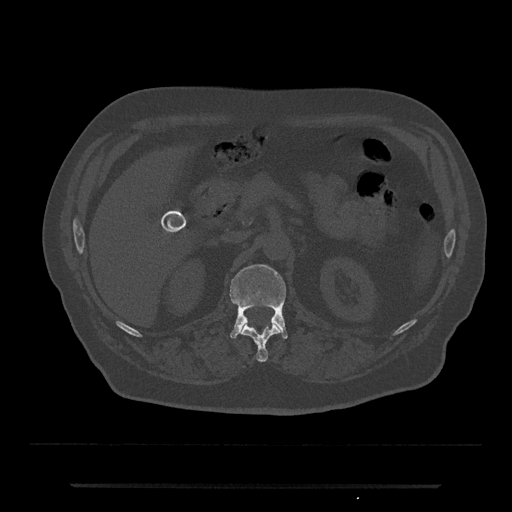
CT including the spine, one axial slice; position 559 of 797 along the scan axis; 120 kVp; bone window (W 1800 / L 400 HU); 0.5 mm slice thickness; 512 × 512 image matrix, field of view 434 × 434 mm. Male patient, age 80 years. Case-level facts recorded for this patient, not image findings: primary cancer: prostate; vertebrae with lytic lesions (as recorded): L1, T11.
Structures marked on this image (semi-automatic segmentation, software-assisted and operator-edited):
- L1 vertebra: bounding box <230,265,288,339> (left, top, right, bottom; pixels)
- T12 vertebra: <242,324,280,362>